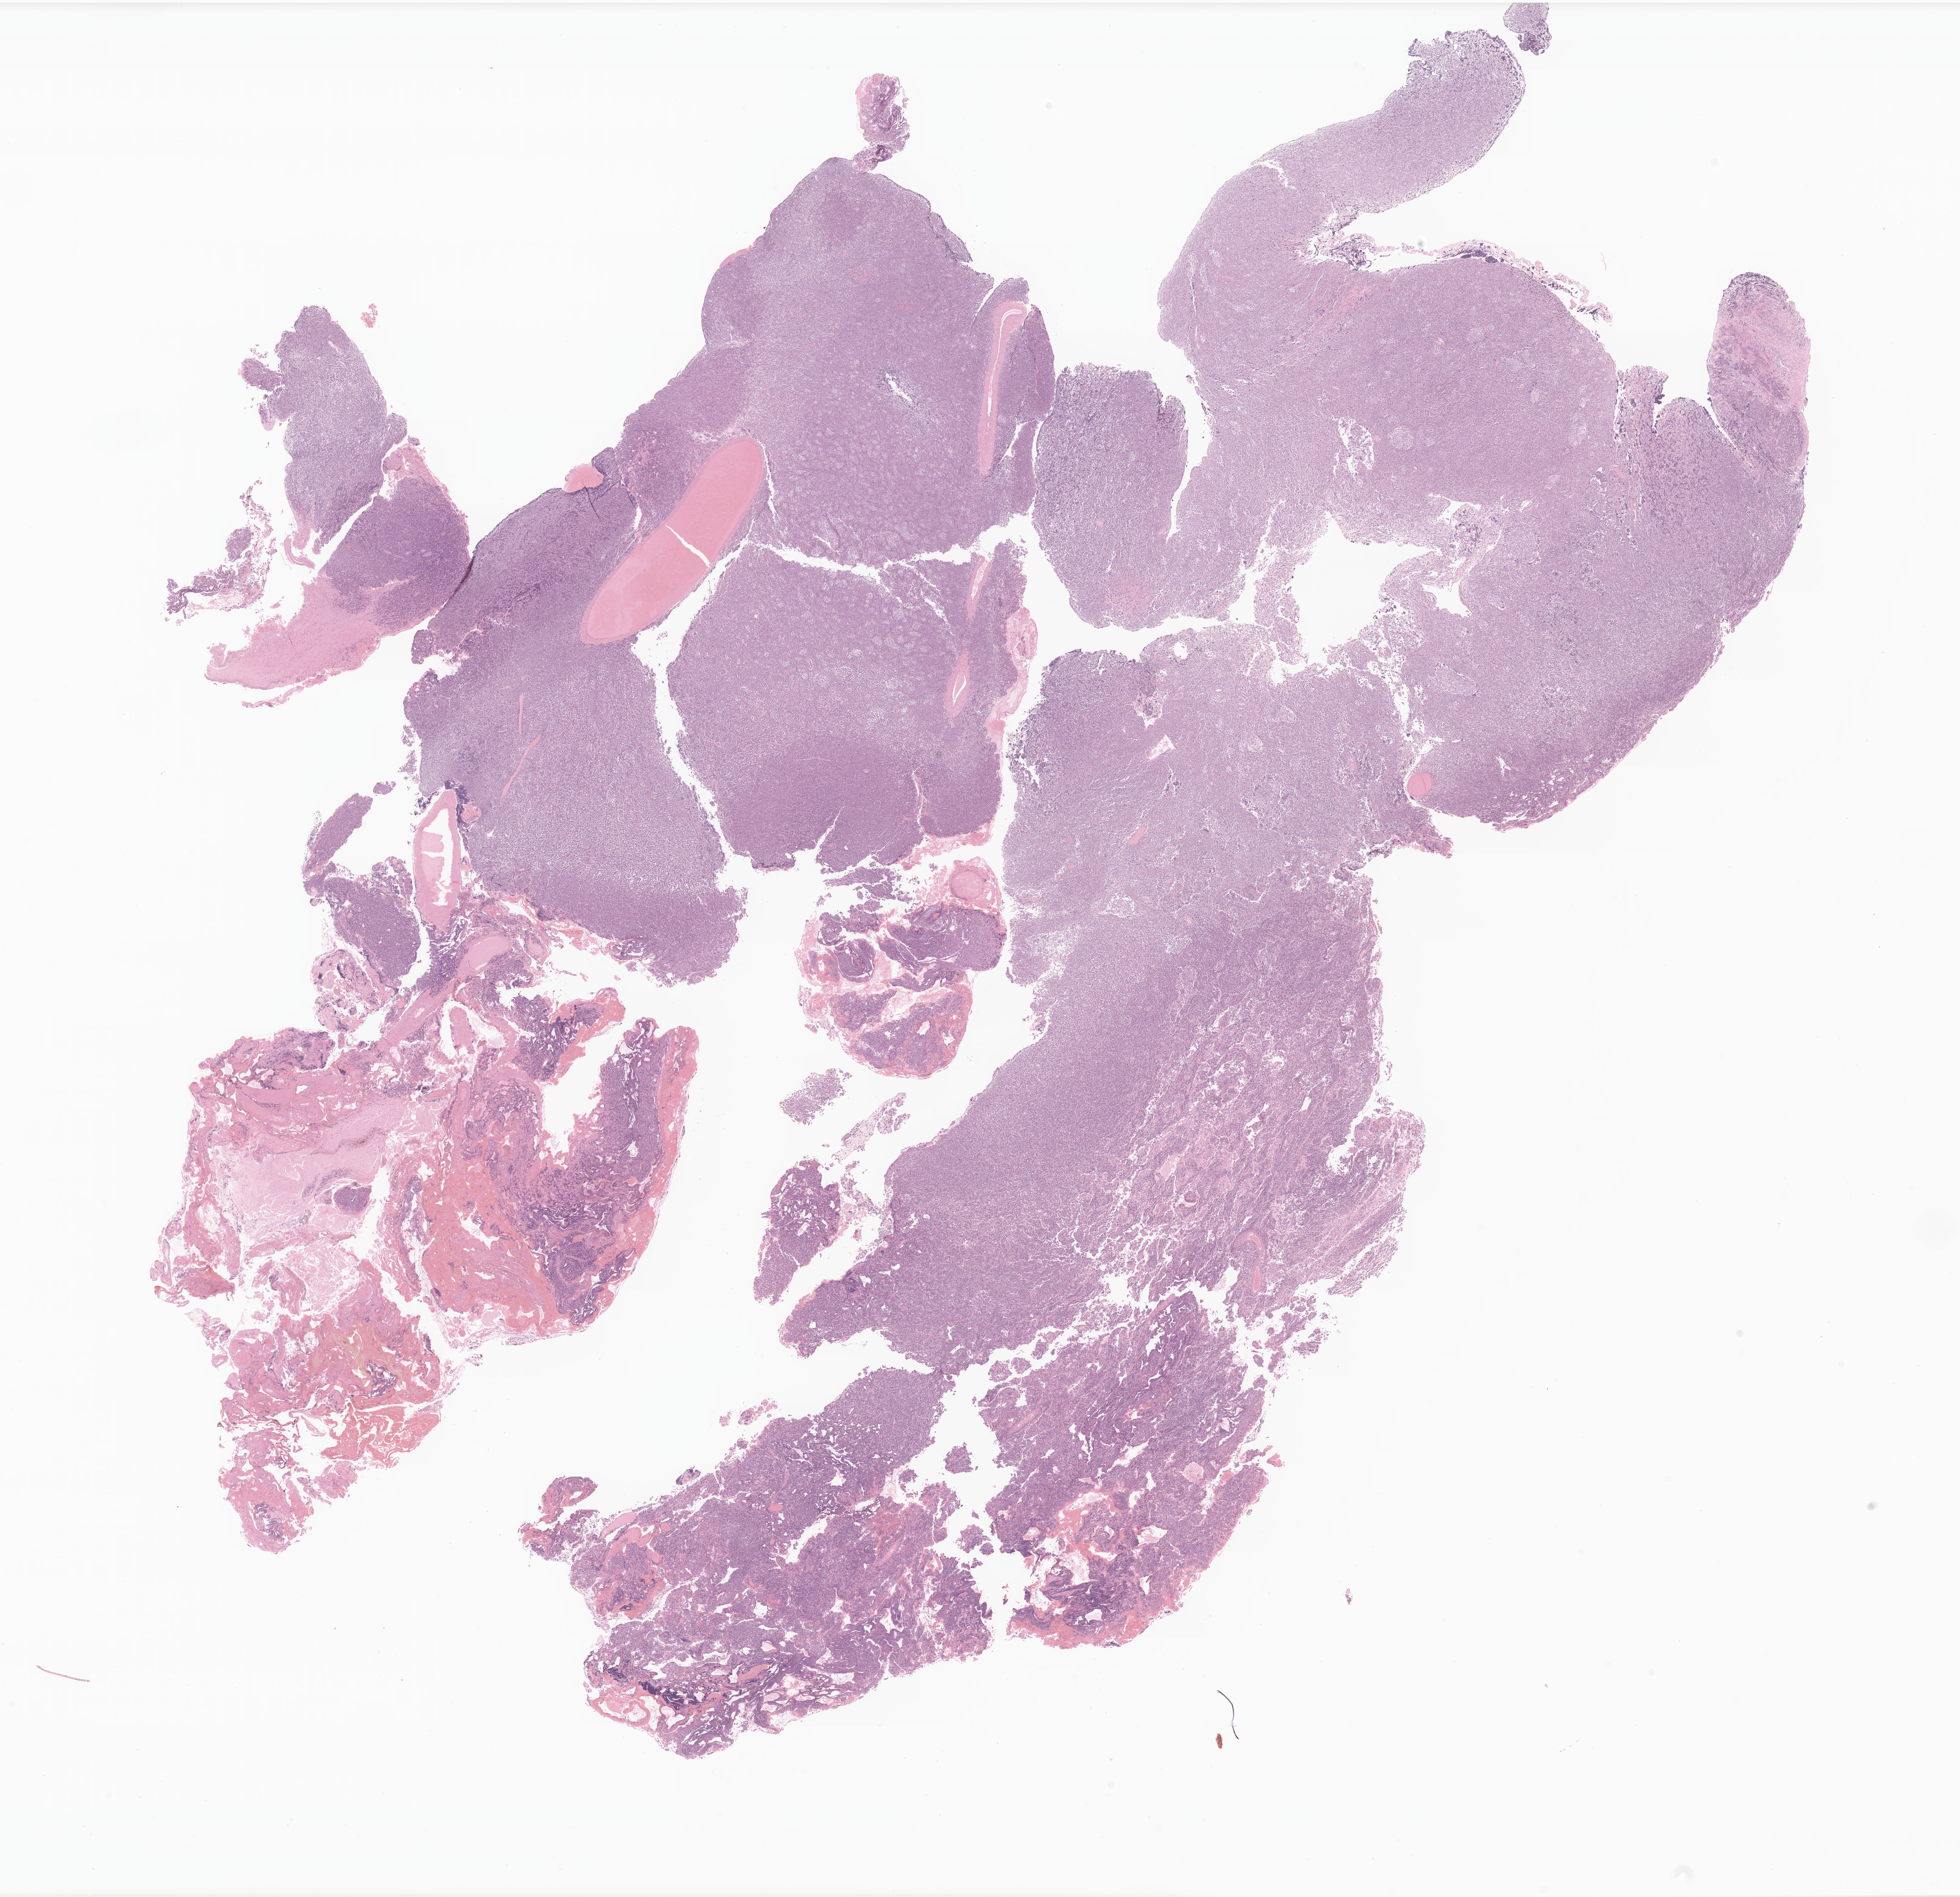
Digitized haematoxylin and eosin-stained section of tumor tissue from the cerebellum, low-resolution overview of the scanned area, about 24.0 x 23.2 mm, formalin-fixed, paraffin-embedded (FFPE) tissue. Patient male; age 130 months (10 years 10 months).
- diagnosis (ICD-O-3 morphology term): Medulloblastoma, NOS